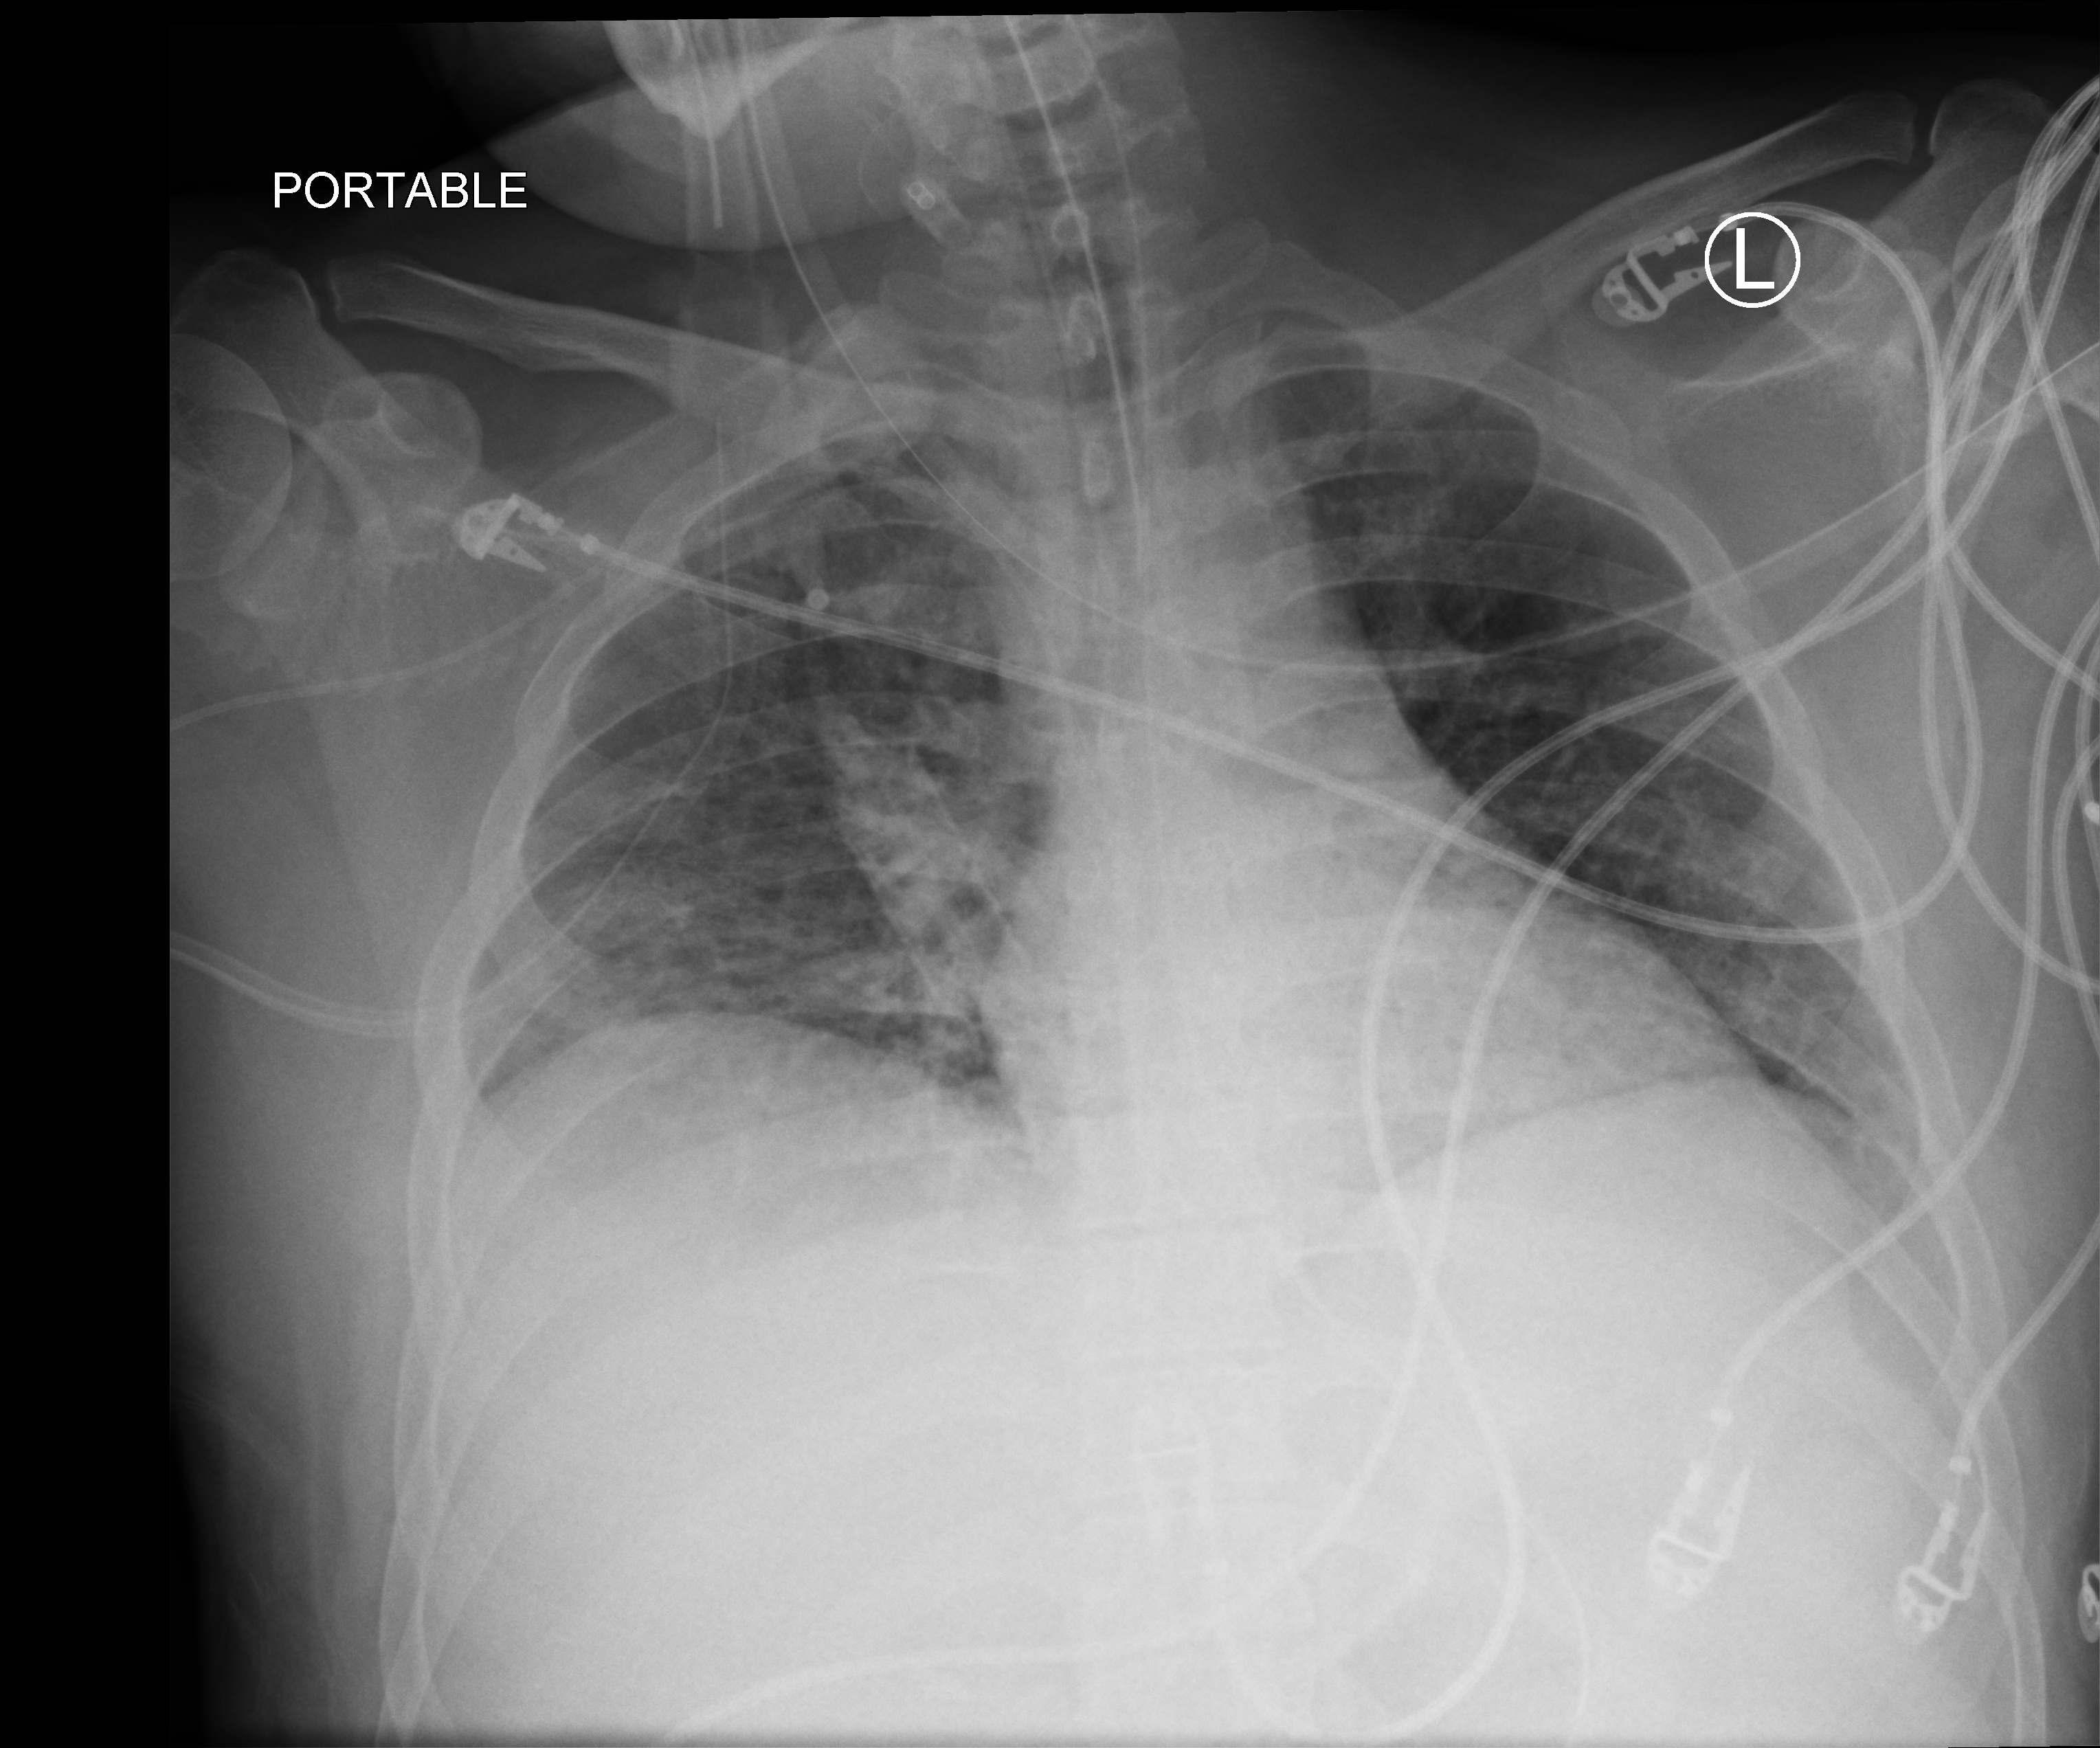
Bedside chest radiograph (computed radiography), anteroposterior (AP) projection. Patient hospitalised with COVID-19; male, aged 18–59 years.
Admission-level facts for this patient (not findings on this image; timing relative to this image not recorded):
- admitted to intensive care during this hospital stay: yes